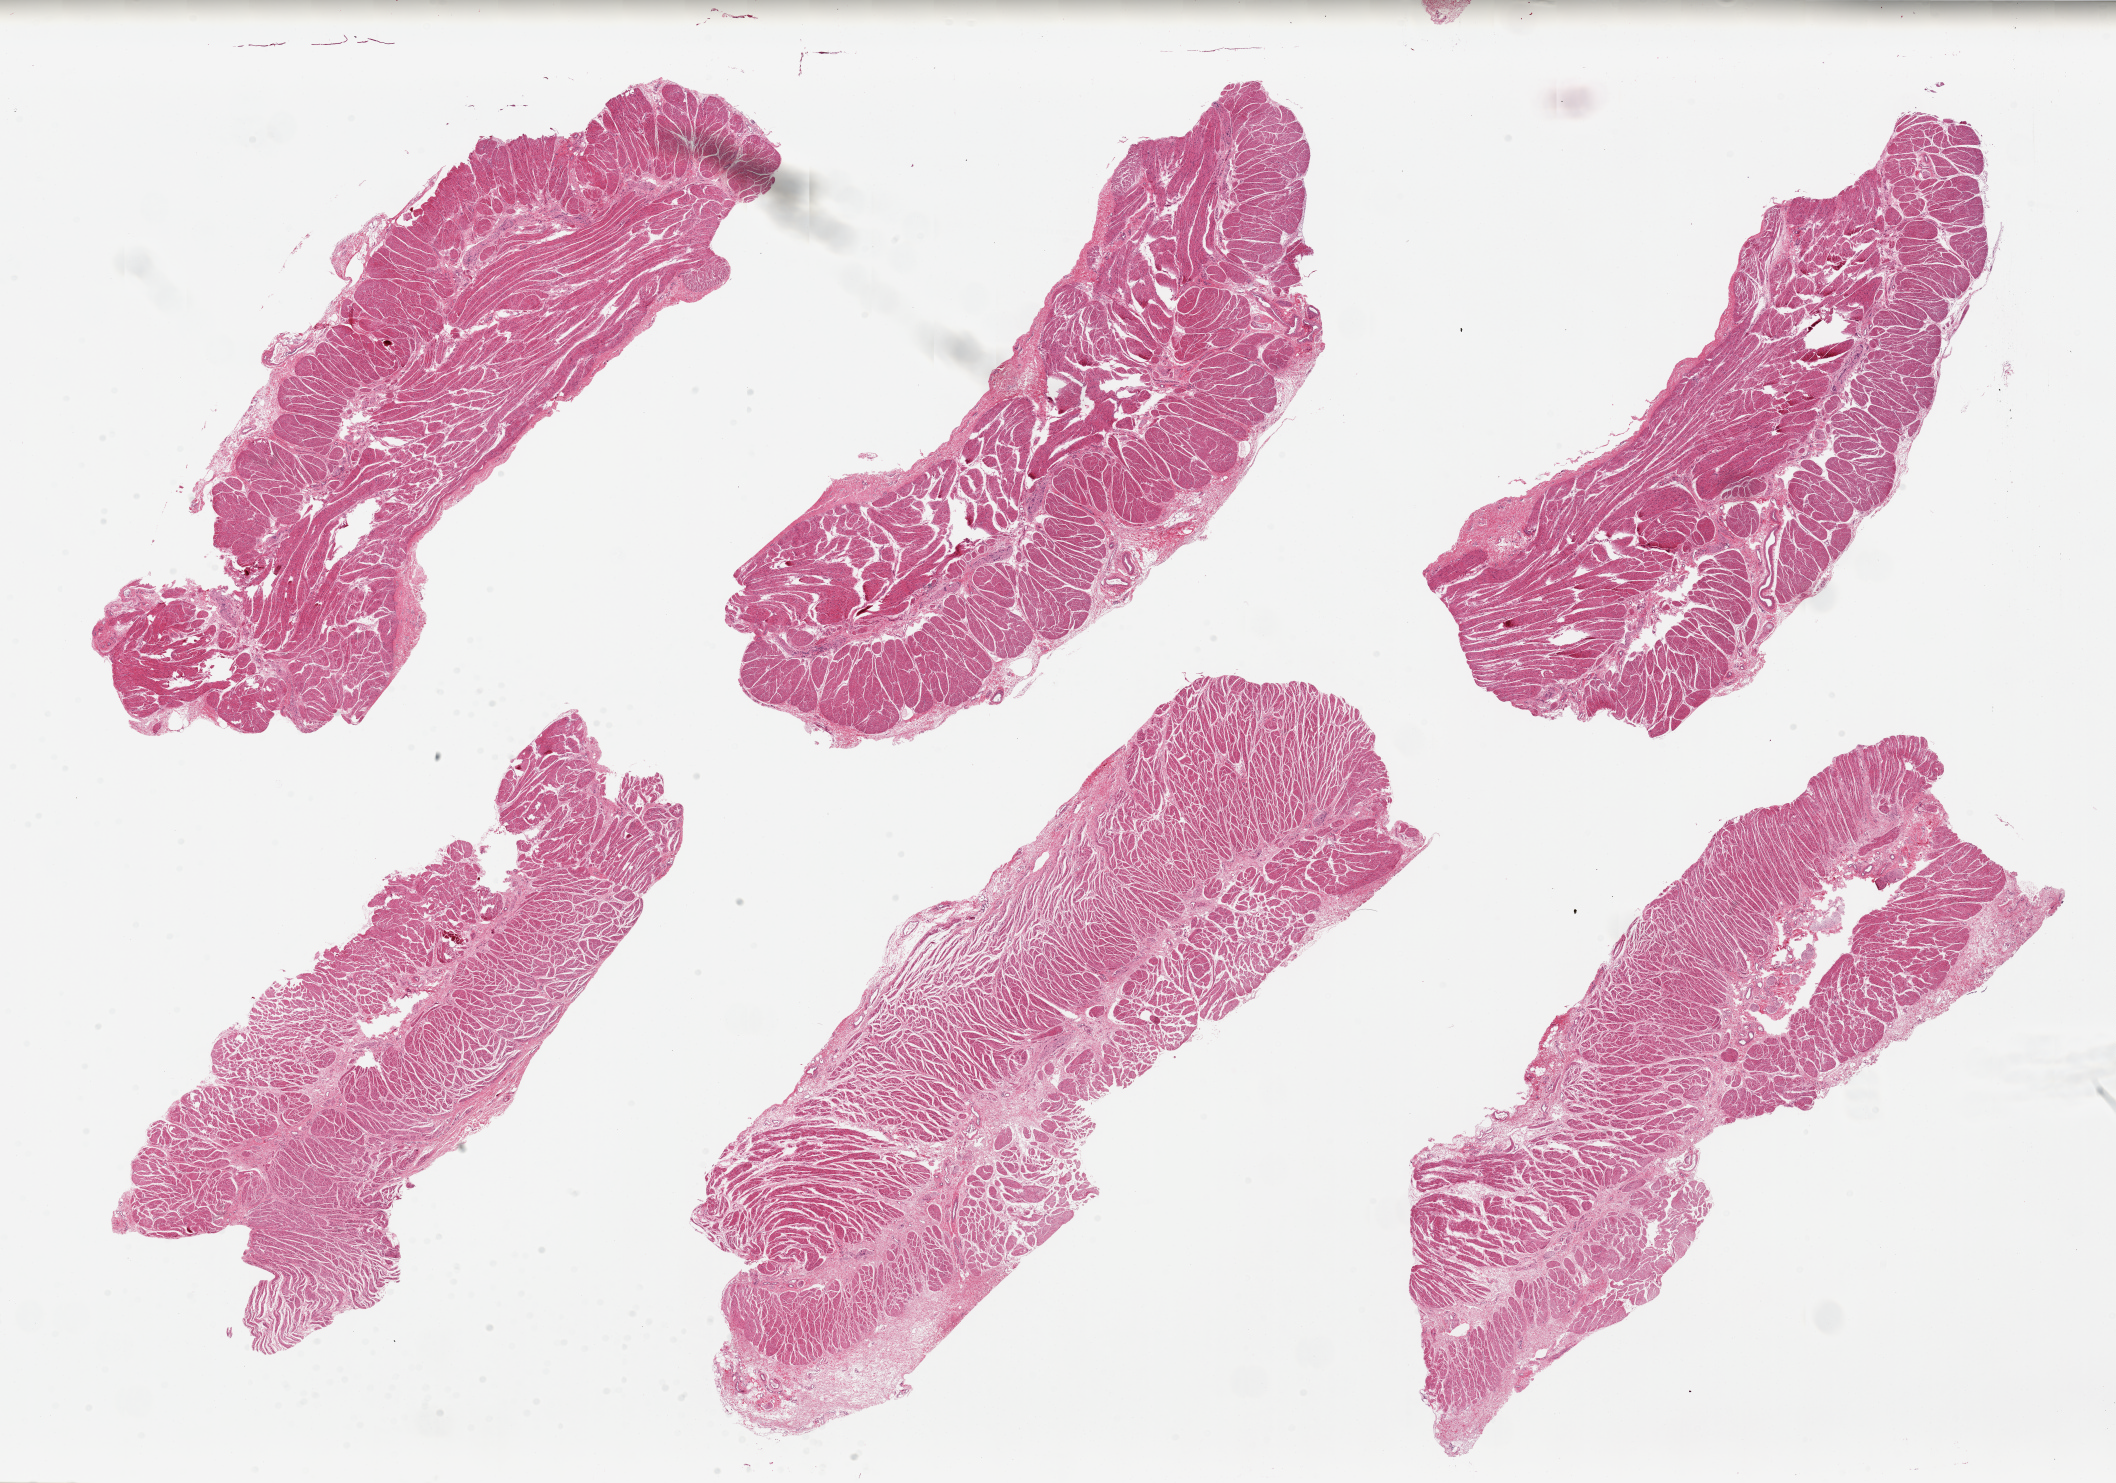
Digitized H&E-stained section, low-resolution overview of the scanned area, about 33.5 x 23.5 mm (slide scanned at 20x); PAXgene-fixed paraffin-embedded (PFPE) section; target tissue: gastroesophageal junction; tissue donor sample. Donor: male.
Reviewer comment on this tissue sample: 6 pieces, up to 15x5.5mm.Well trimmed.